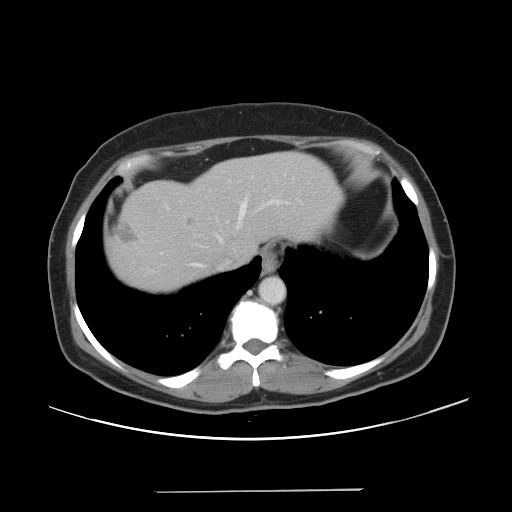
Contrast-enhanced abdominal CT, one axial slice; slice 40 of 56 in the series (ordered by position); intravenous contrast given; soft-tissue window (W 400 / L 40 HU); 5 mm slice thickness; 512 × 512 image matrix. Female patient, age 54 years. Case-level facts recorded for this patient, not image findings: diagnosis: colorectal cancer liver metastases, imaged before liver resection; multiple liver metastases: yes; largest metastasis: 3.2 cm; chemotherapy before resection: yes.
Structures marked on this image (manually delineated by an expert):
- hepatic veins: box from (x=148, y=196) to (x=287, y=272) px
- liver: (x=111, y=152)–(x=343, y=293)
- planned liver remnant (the part of the liver to remain after resection): (x=202, y=152)–(x=342, y=265)
- liver metastasis: (x=118, y=220)–(x=137, y=243)
- liver metastasis: (x=186, y=217)–(x=195, y=226)